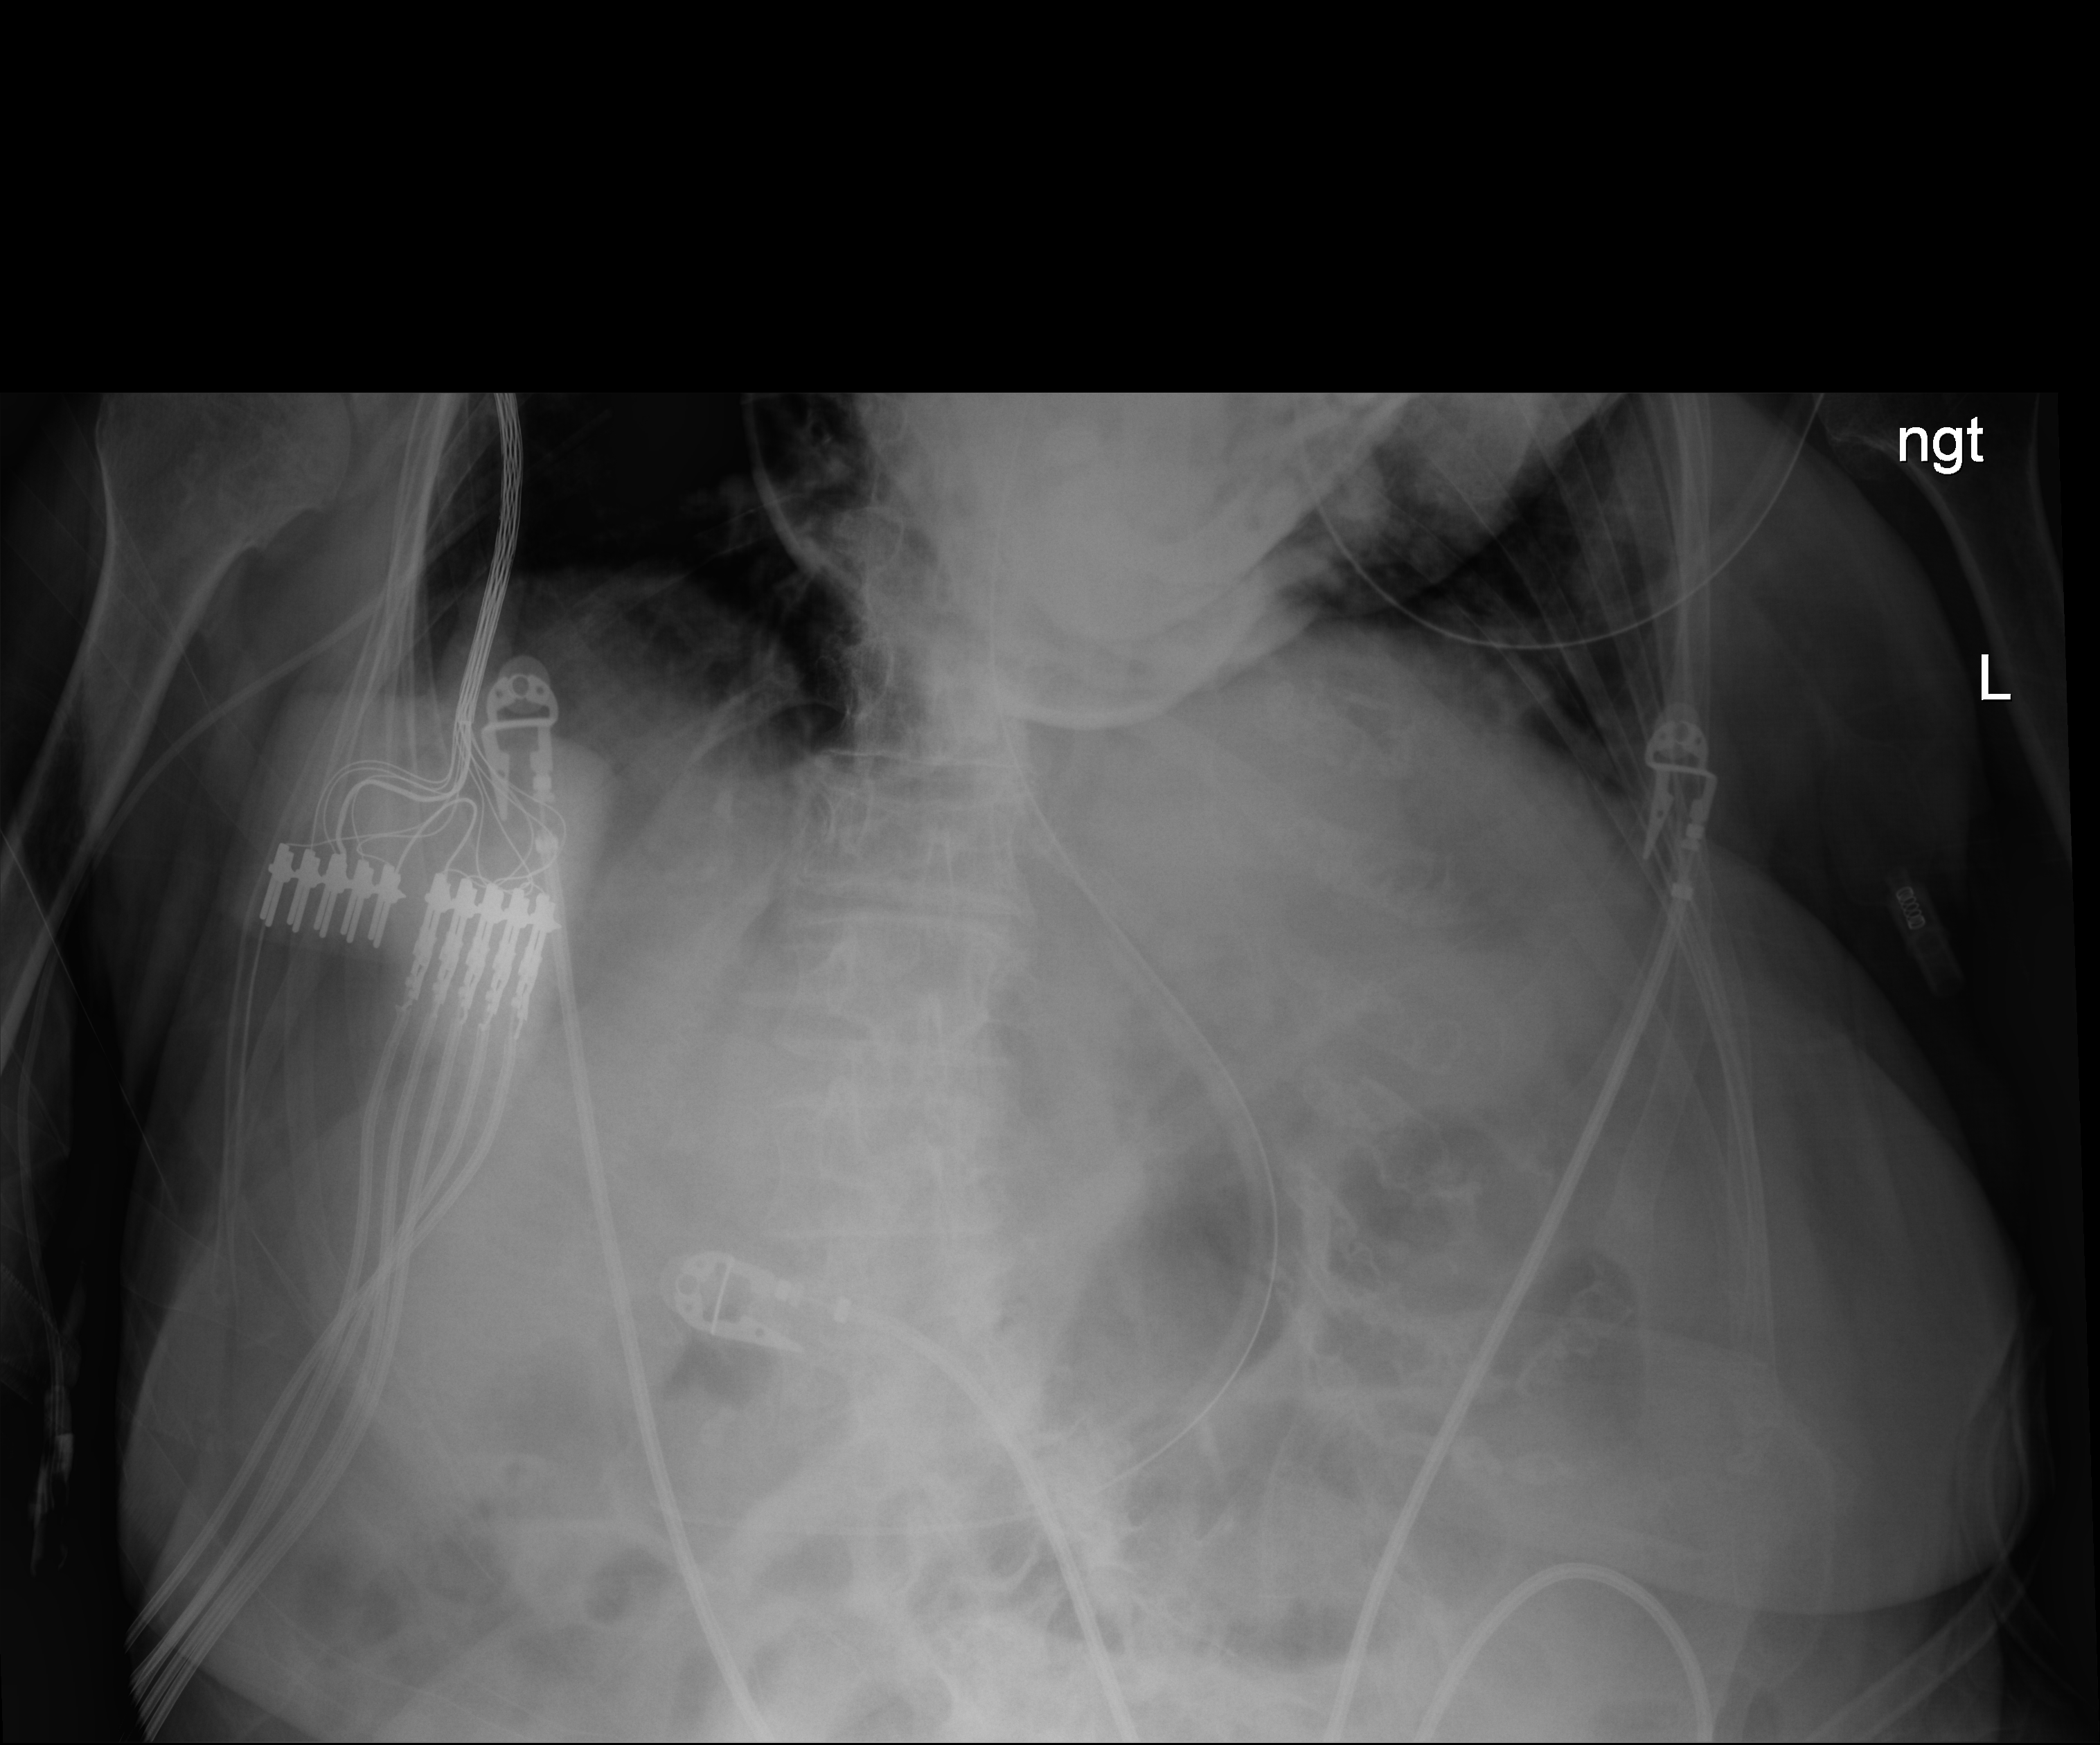
Bedside abdomen radiograph (digital radiography); anteroposterior (AP) projection. Female patient hospitalised with COVID-19, age 75–90 years.
Admission-level facts for this patient (not findings on this image; timing relative to this image not recorded): admitted to intensive care during this hospital stay: yes; mechanically ventilated during this hospital stay: yes.